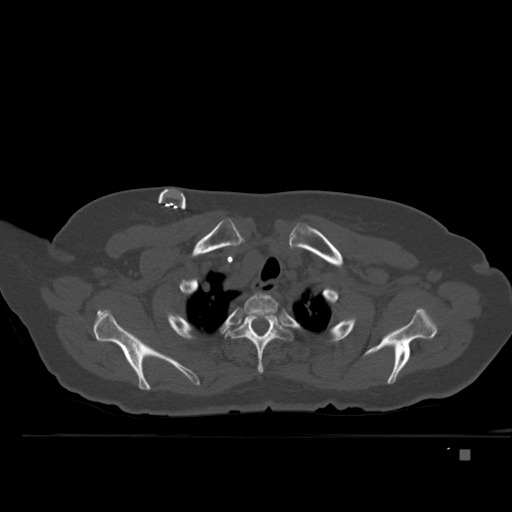
CT including the spine, one axial slice; position 394 of 477 along the scan axis; bone window (W 1800 / L 400 HU); 512 × 512 image matrix, field of view 422 × 422 mm. Female patient, age 74 years. Case-level facts recorded for this patient, not image findings: primary cancer: colon.
Outlined on this slice (semi-automatically segmented with operator editing):
- T1 vertebra: bounding box [x1, y1, x2, y2] px = [229, 293, 278, 325]
- T2 vertebra: [221, 308, 298, 374]